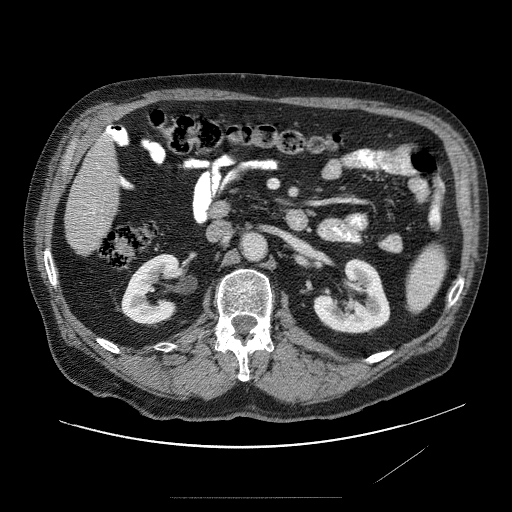
Contrast-enhanced abdominal CT (liver protocol), one axial slice. Position 15 of 89 along the scan axis. 120 kVp. Soft-tissue window (W 400 / L 40 HU). 2.5 mm slice thickness. 512 × 512 image matrix. From the clinical record (not read from this slice): diagnosis: hepatocellular carcinoma (patient treated with transarterial chemoembolisation; whether this scan precedes or follows treatment is not stated here); TNM stage (as recorded): Stage-IVA; Child-Pugh class: A; tumour nodularity: multinodular.
Structures marked on this image (semi-automatic segmentation, software-assisted and operator-edited):
- liver parenchyma outside the tumour (the mass and vessels are separate outlines, so this box may not span the whole liver): box from (x=64, y=130) to (x=128, y=260) px
- liver vessels: (x=93, y=154)–(x=116, y=219)